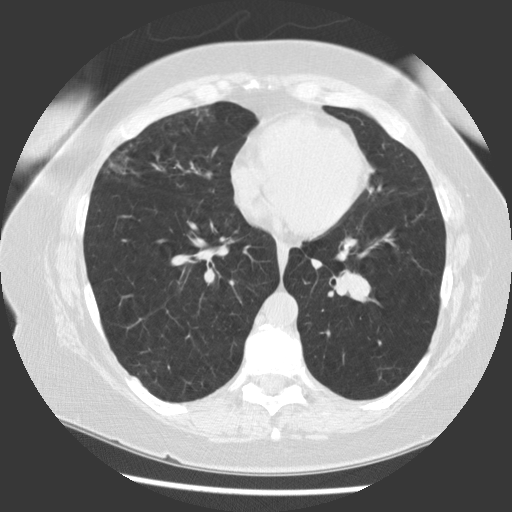
Chest CT (low-dose screening protocol), one axial image. Baseline screening round. Lung window (W 1500 / L -600 HU). Standard (soft-tissue) reconstruction kernel (STANDARD). Slice 56 of 130 in the series. Female participant, aged 58 years at enrolment. Former smoker at enrolment.
Expert reader's lesion annotation, bounding box [x1, y1, x2, y2] px = [327, 258, 391, 322]. The exam's reader record, not a measurement of the box and not confirmed to be the same lesion: non-calcified nodule or mass ≥4 mm, left lower lobe, 22 × 15 mm, smooth margins, soft tissue attenuation. Participant outcome: lung cancer diagnosed 108 days after this screen — carcinoma, NOS, left hilum, stage IA (AJCC 6th edition), 28 mm at pathology.